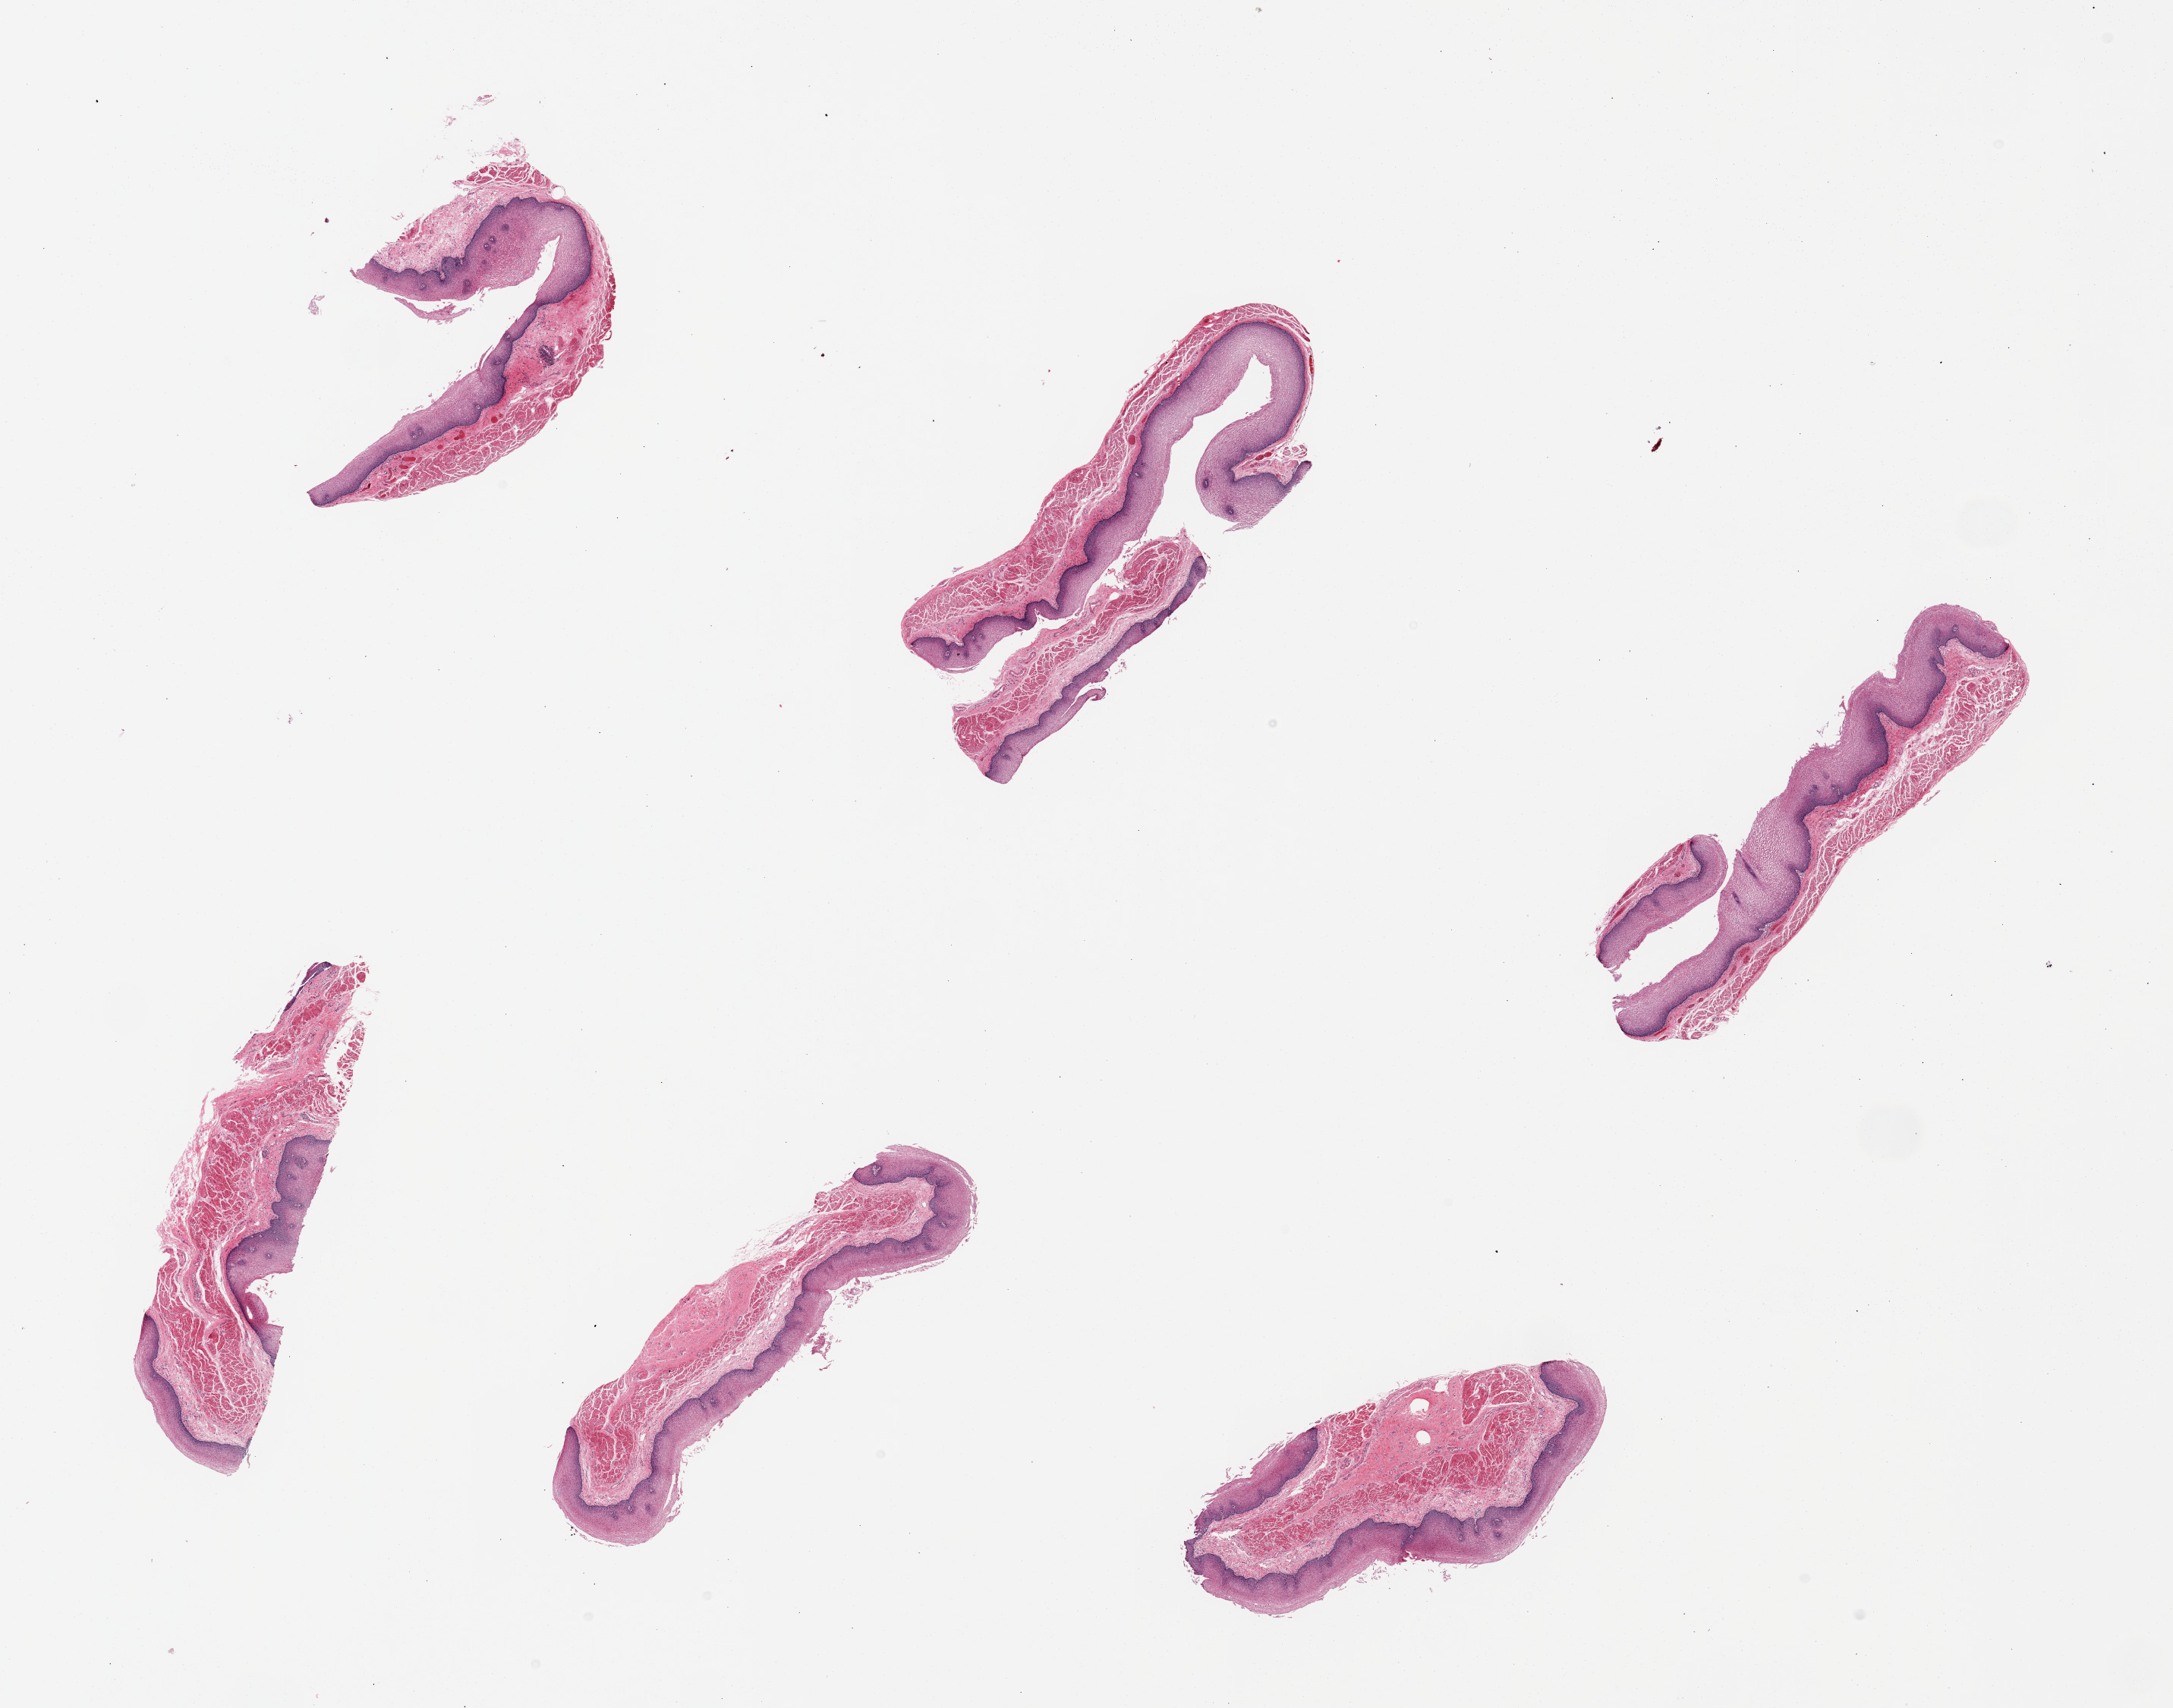
Whole-slide image, hematoxylin and eosin (H&E) stain, a low-resolution overview of the entire scanned area, about 22.6 x 17.8 mm (slide scanned at 20x); PAXgene-fixed paraffin-embedded (PFPE) section; sampled site (target tissue): esophageal mucous membrane; tissue donor sample. Donor: female.
Review note (as recorded): 6 pieces.